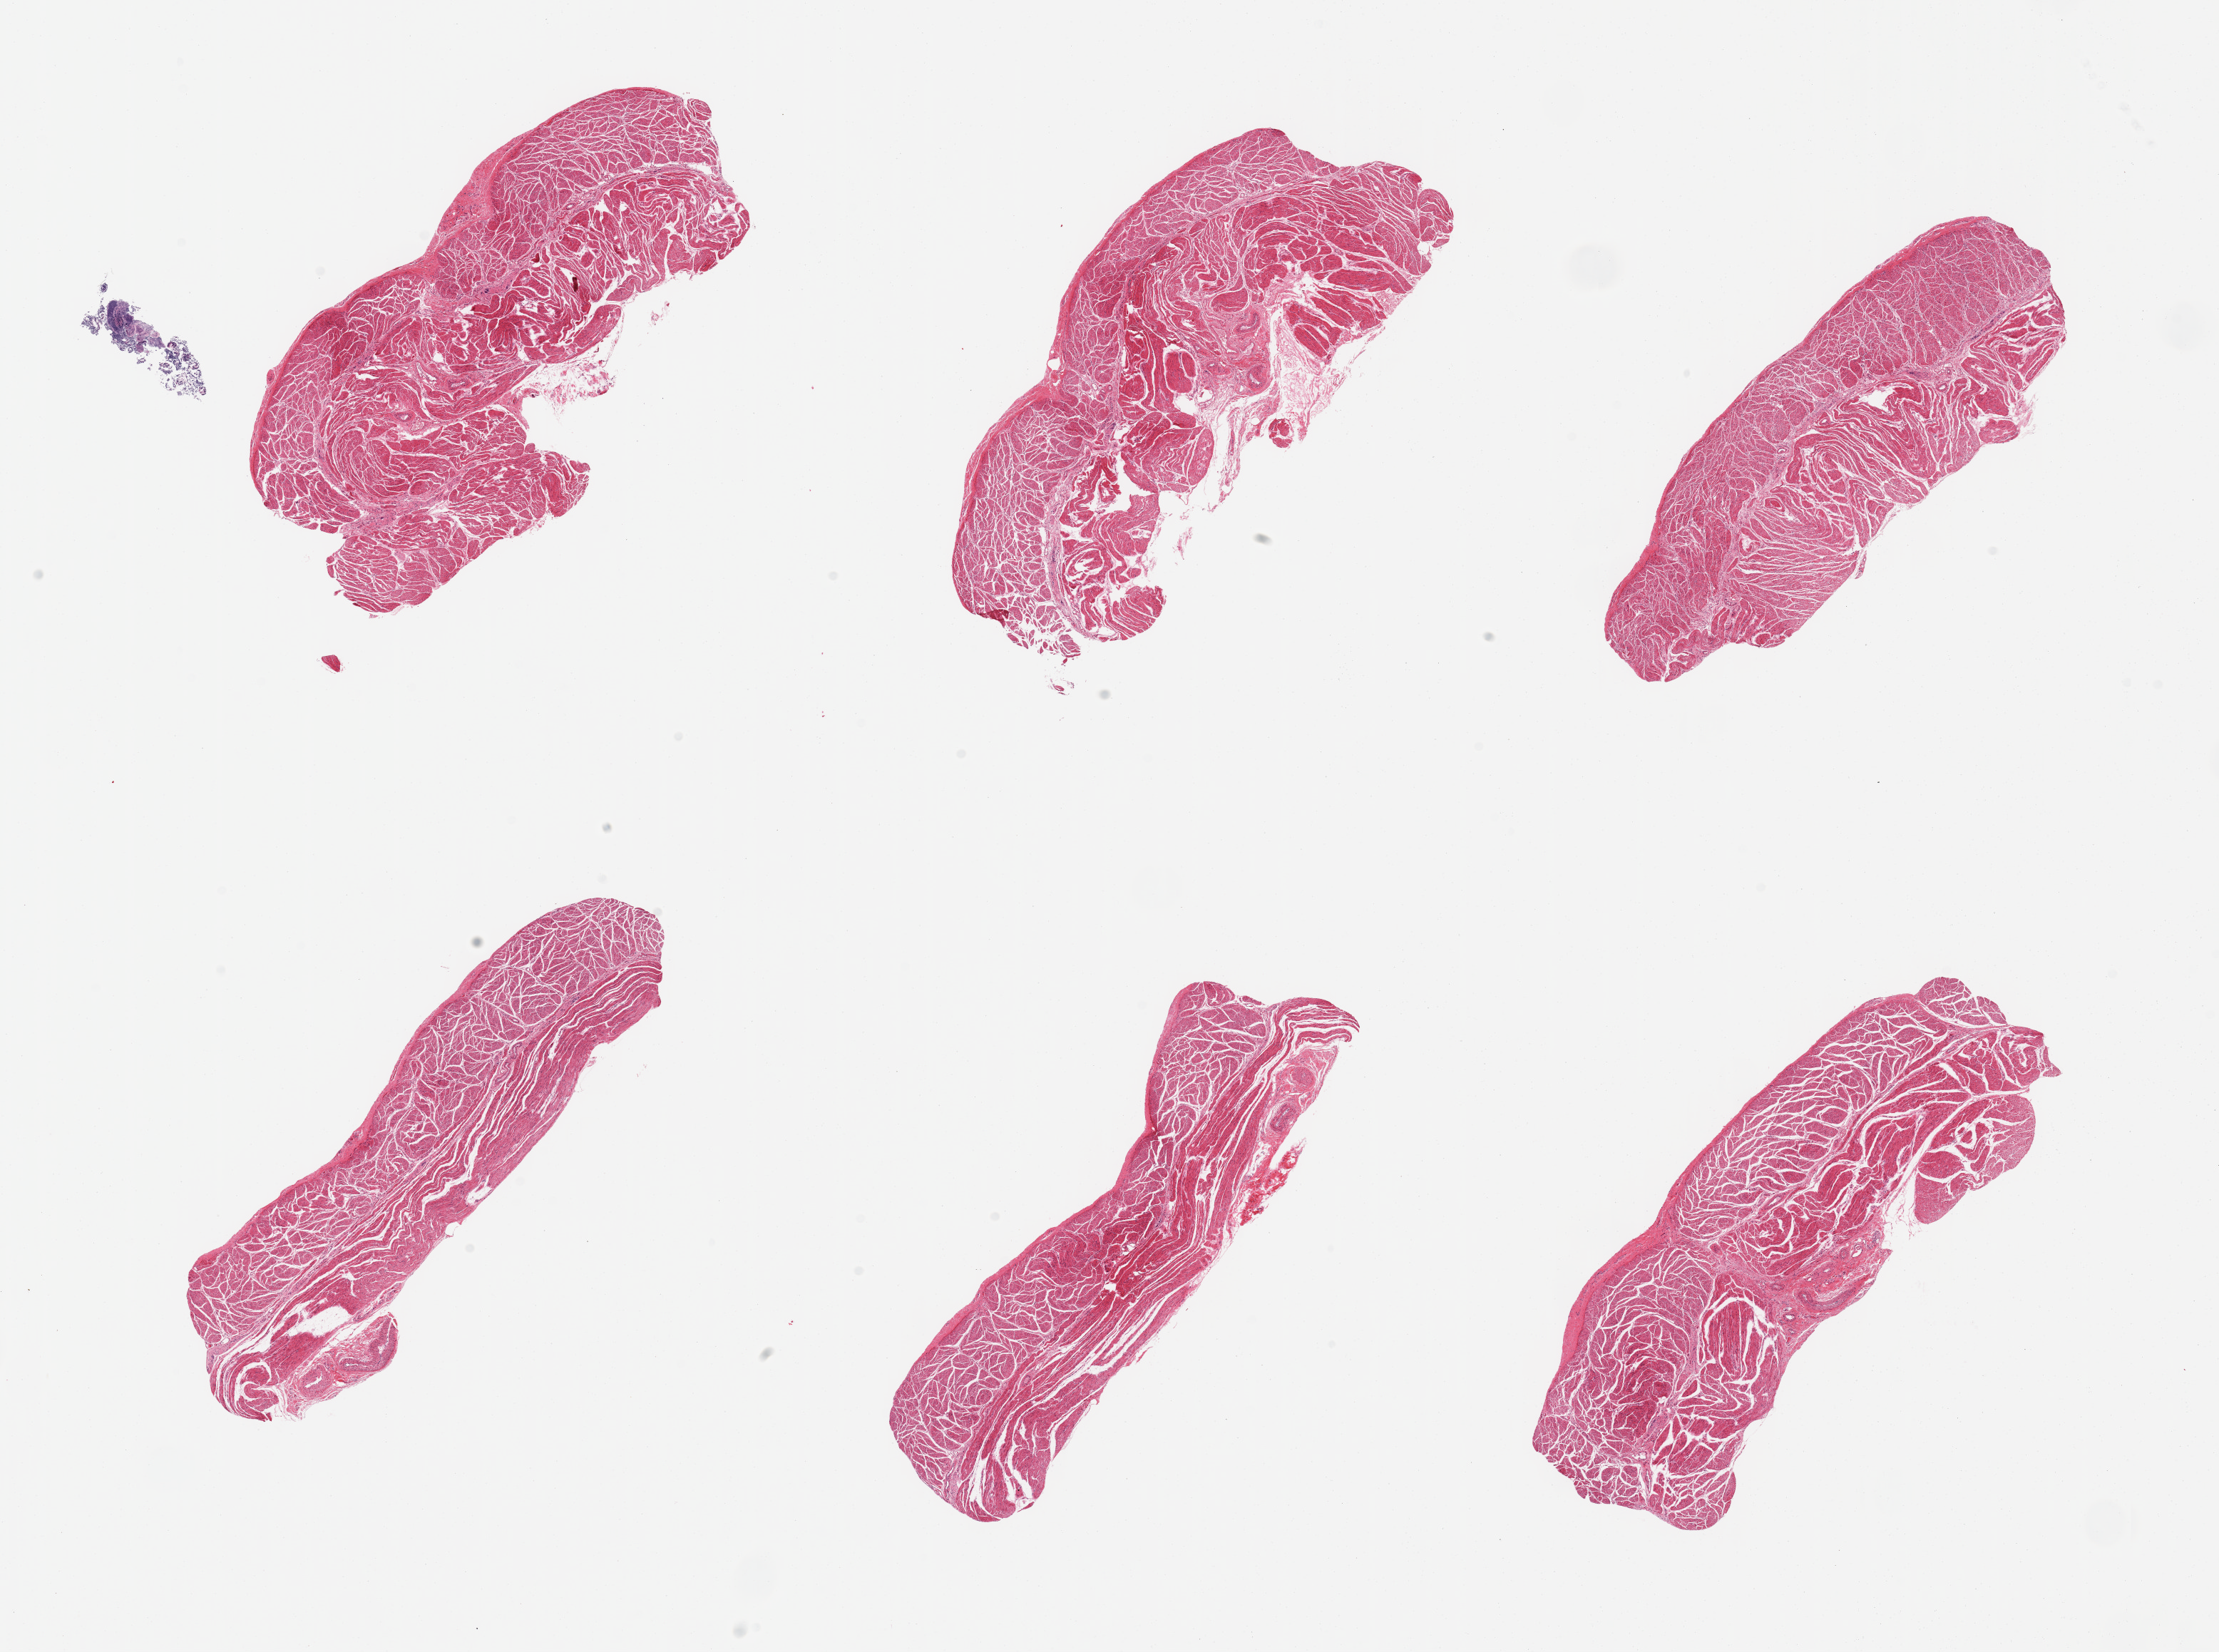
Hematoxylin and eosin (H&E) whole-slide image, whole scanned area (about 24.6 x 18.3 mm) shown as a low-resolution overview; PAXgene-fixed, paraffin-embedded tissue; sampled site (target tissue): esophageal muscle; donor tissue sample. Donor sex: female.
Pathologist's review note for this sample: 6 pieces, all muscularis.